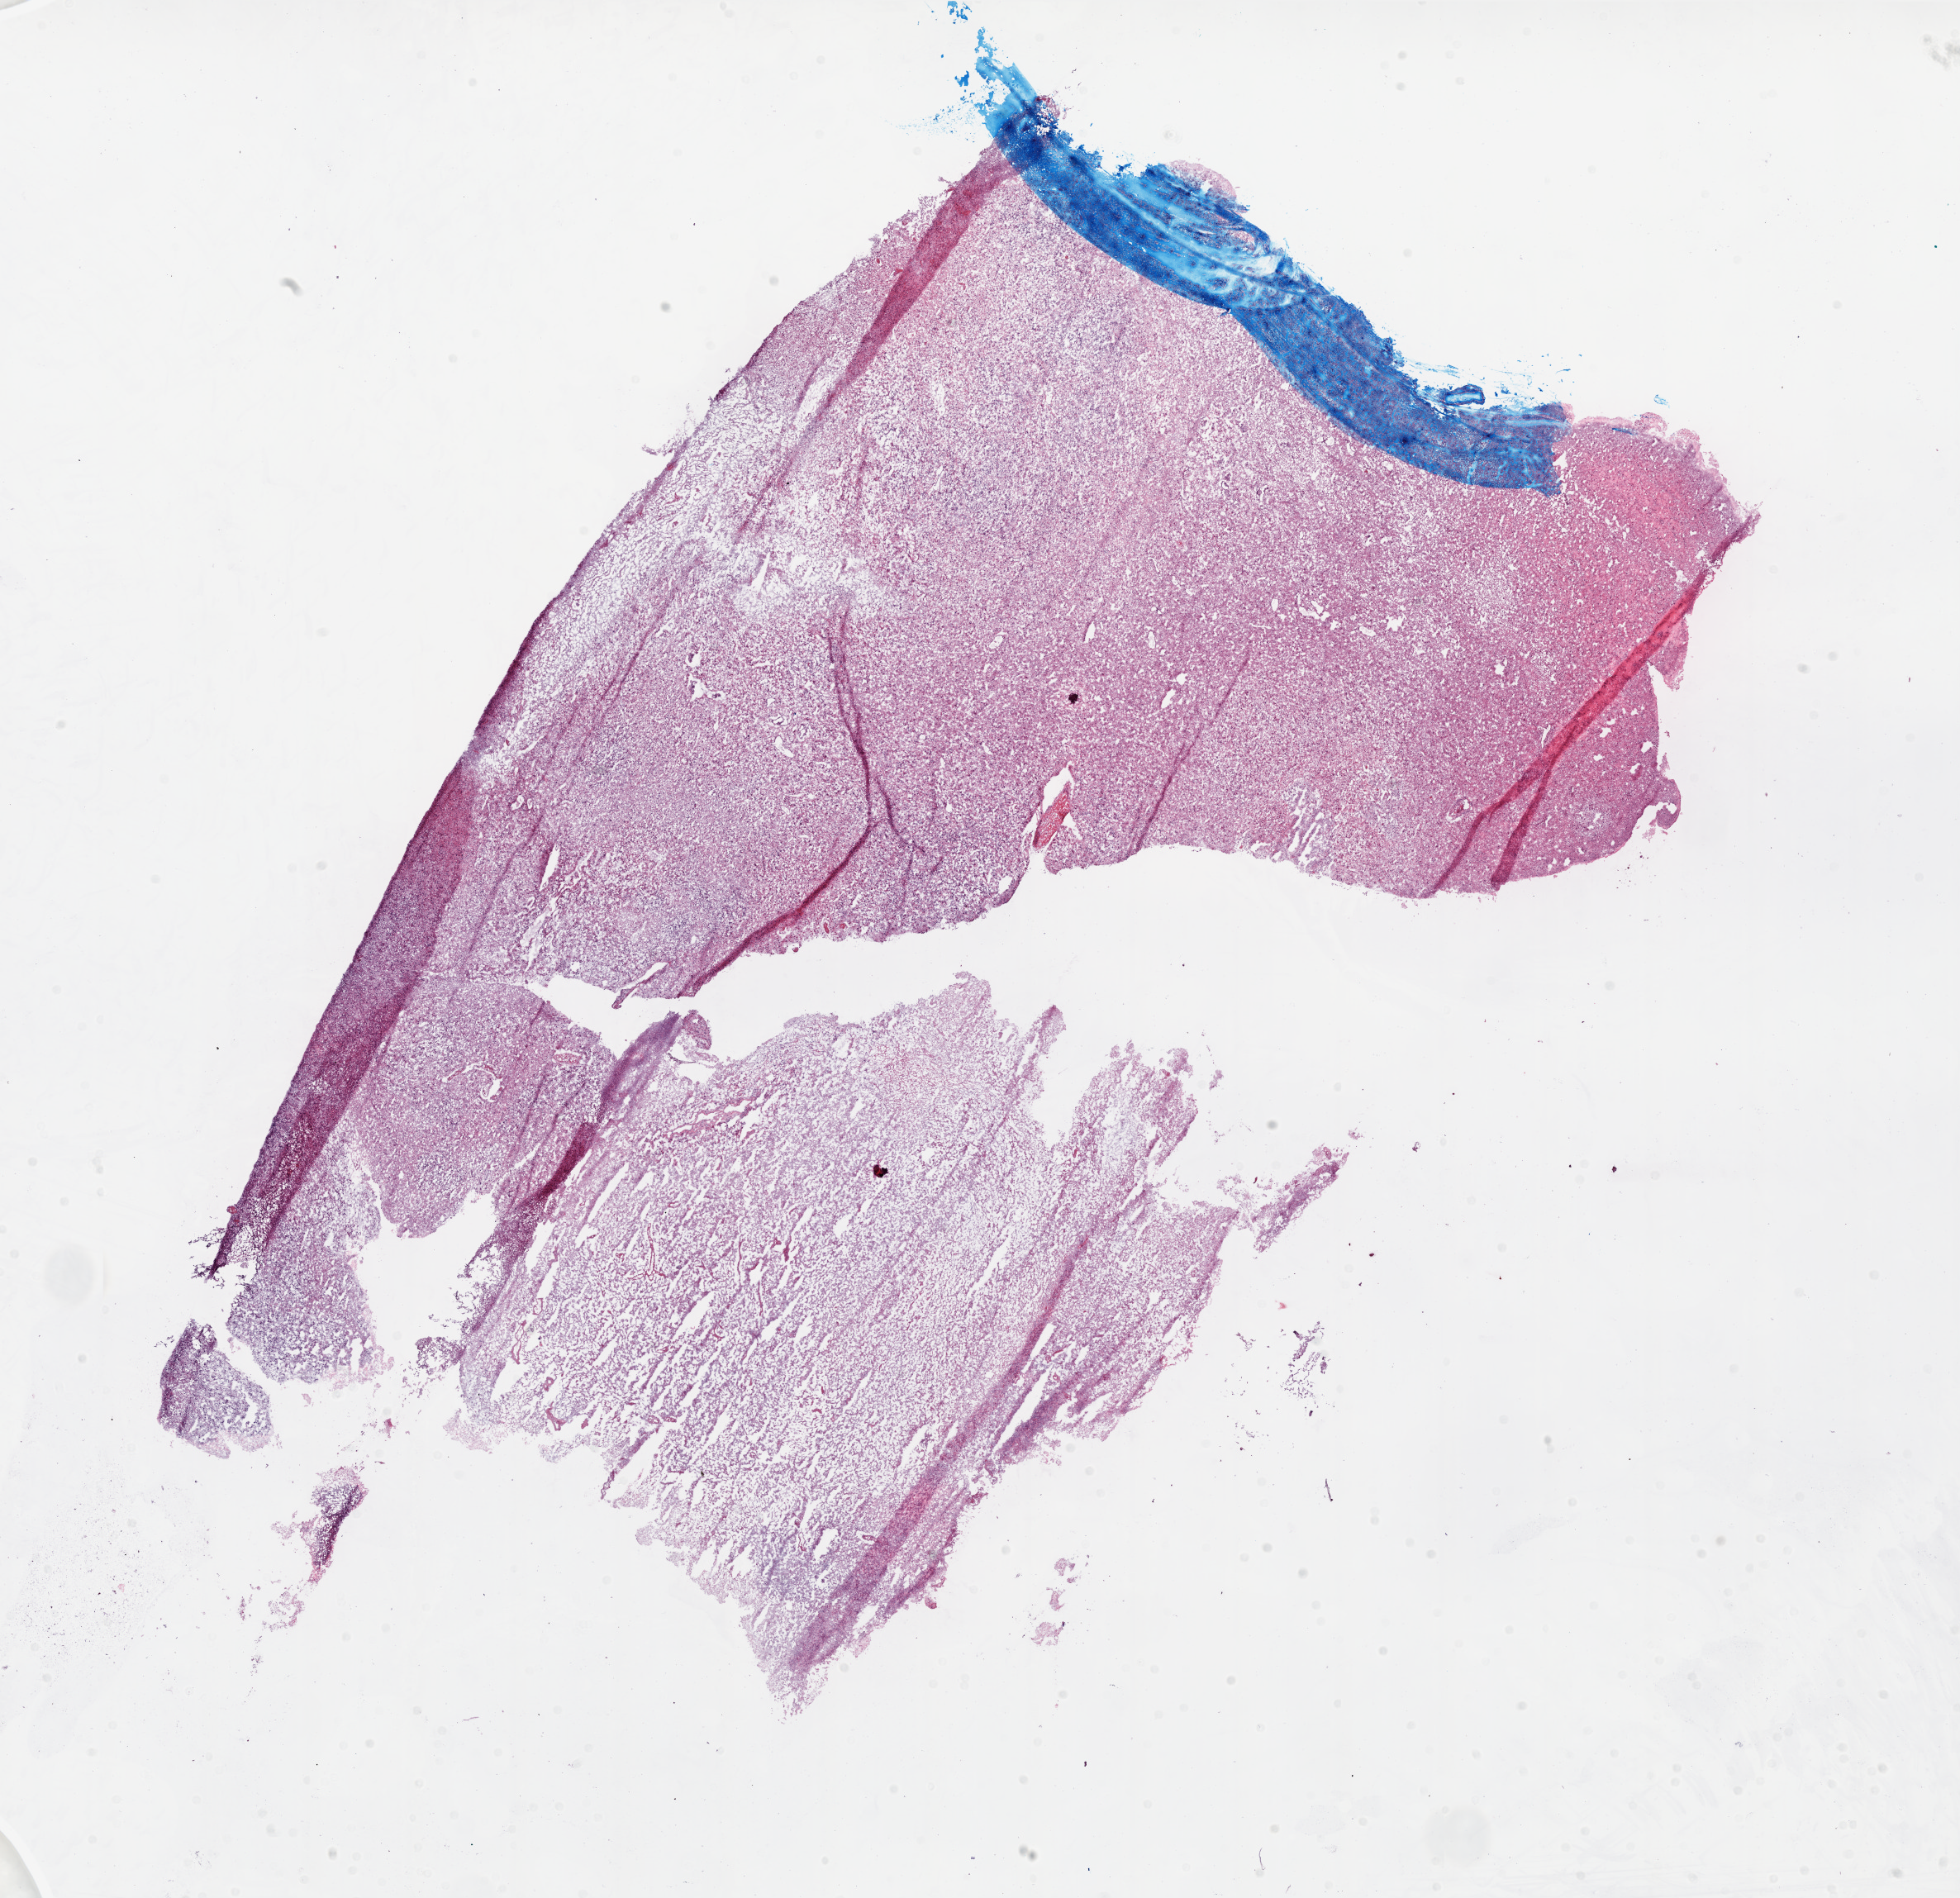
Digitized Hematoxylin and eosin (H&E) stained tissue section (whole slide), shown as a low-resolution overview of the whole scanned area (about 19.0 x 18.4 mm), frozen section from the top of the tissue portion, primary tumour sample from the brain. Female, age 70 years at initial diagnosis. Pathologist review of this section (percent, as recorded): tumour cells 40%, tumour nuclei 90%, normal cells 0%, stromal cells 20%, necrosis 40%. Infiltration values recorded for this section: lymphocyte infiltration 0%.
Pathologic diagnosis: Glioblastoma.